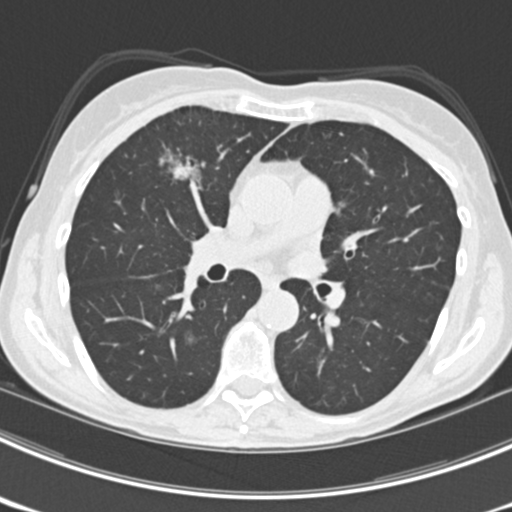
Low-dose screening chest CT, axial slice, third annual screen, lung window (W 1500 / L -600 HU), 2 mm slice thickness, standard (soft-tissue) reconstruction kernel (B30f), 512 × 512 image matrix. Female participant, aged 63 years at enrolment. Current smoker at enrolment.
Expert-annotated lung lesion, box from (x=152, y=138) to (x=218, y=198) px. The screening reader recorded 9 non-calcified nodules or masses ≥4 mm on this exam; which of them this box marks is not recorded.